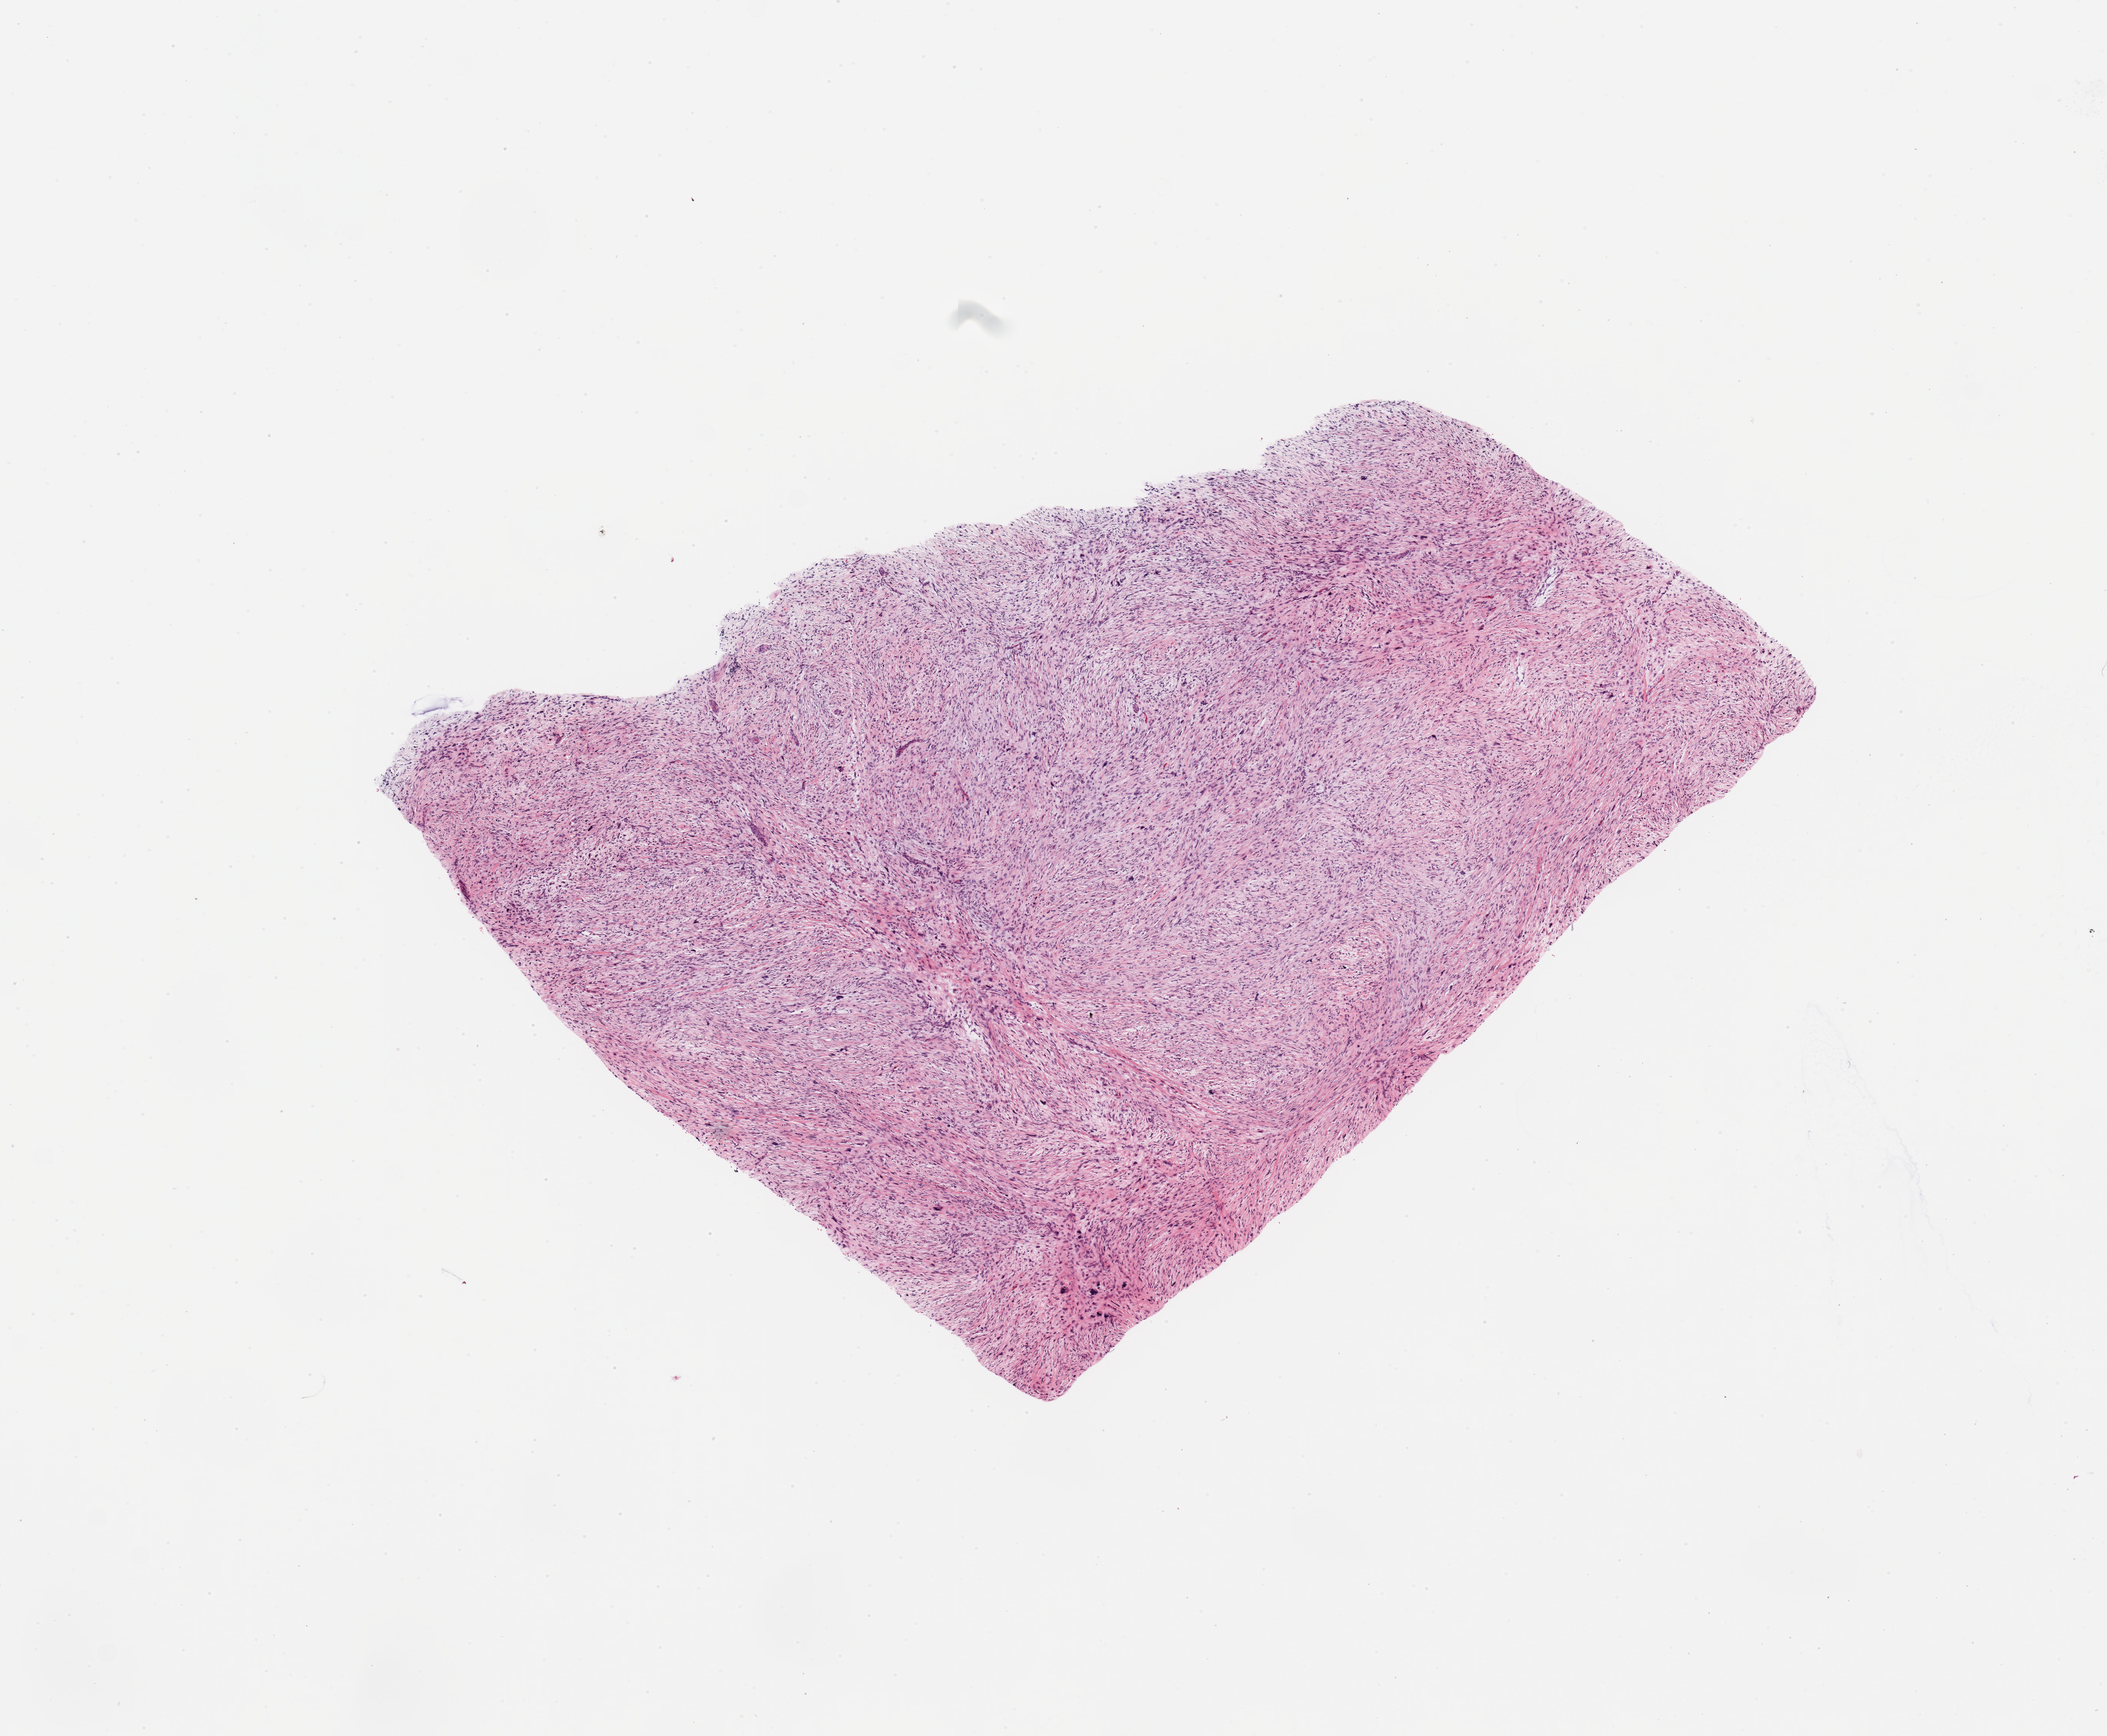
Whole-slide histology image, Hematoxylin and eosin (H&E) stained, a low-resolution overview of the entire scanned area, about 10.8 x 8.9 mm (acquisition: 20x scan). Tumour tissue sample. Patient: male, age 65 years.
Primary tumour site (as recorded): retroperitoneum. Patient diagnosis (cohort enrolment): sarcoma (site not recorded at cohort level).